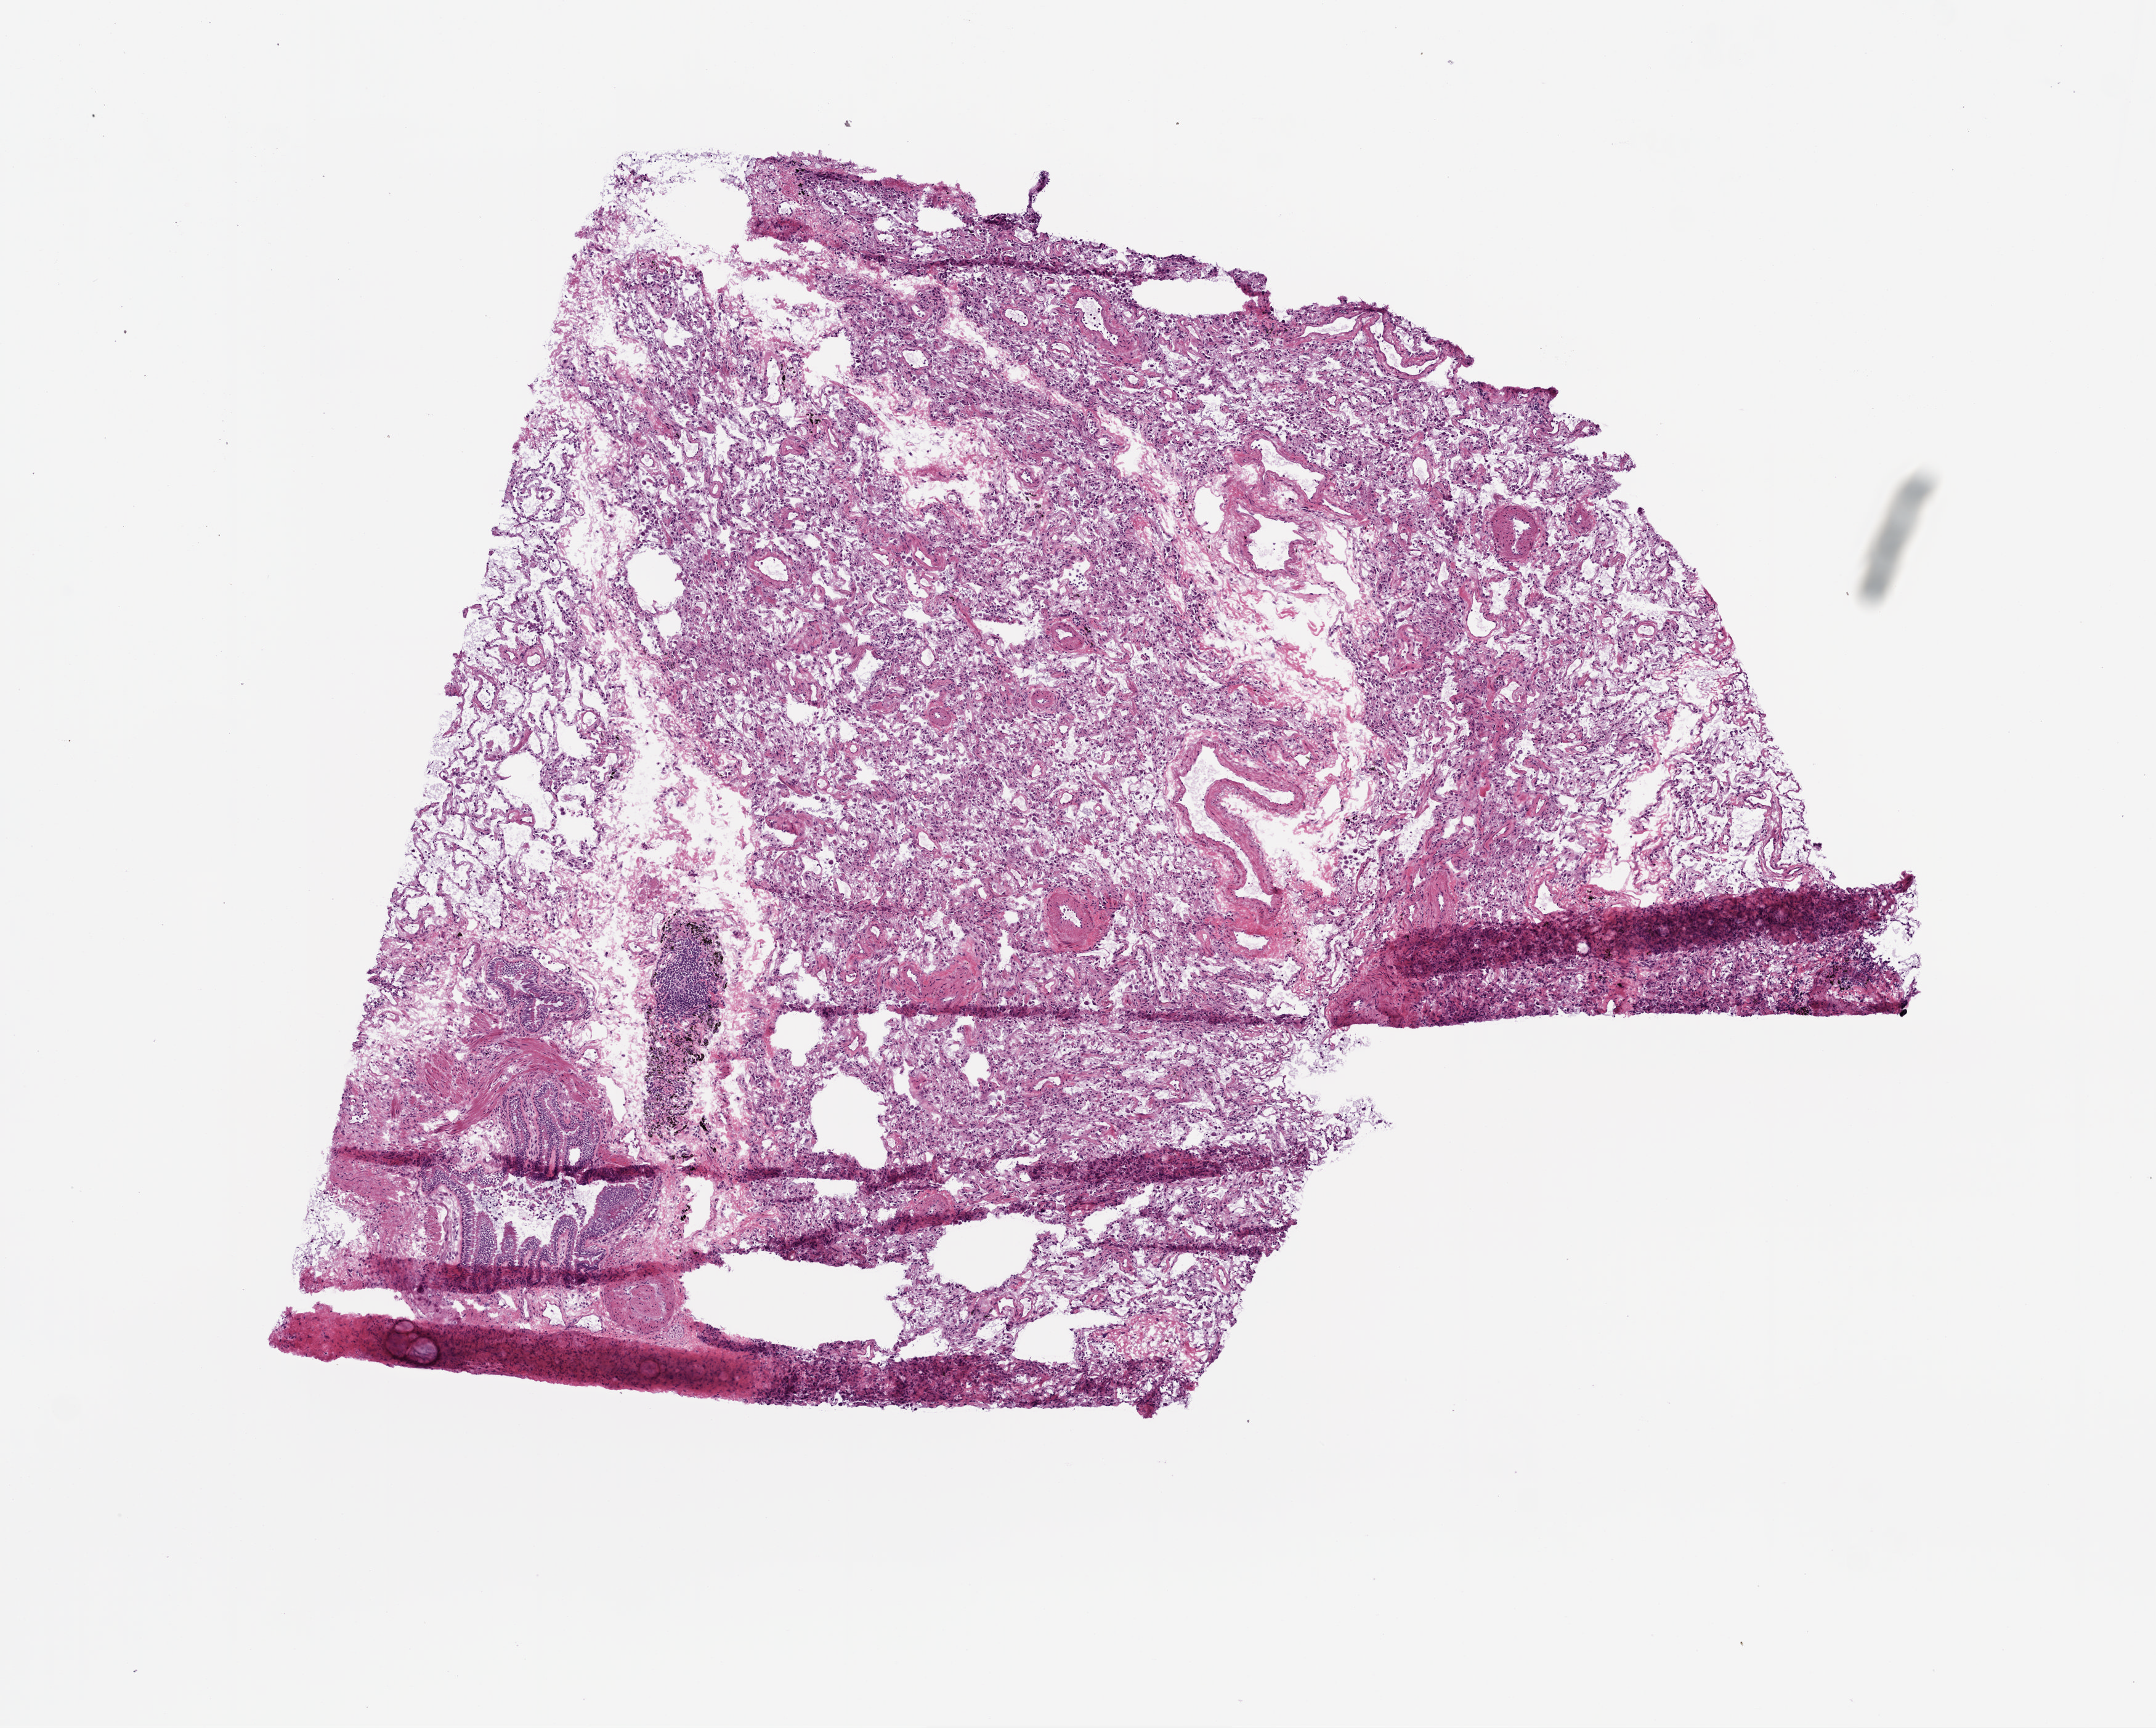
Digitized Hematoxylin and eosin (H&E) stained tissue section (whole slide) — low-resolution overview of the scanned area, about 7.0 x 5.6 mm; frozen section from the top of the tissue portion; solid tissue normal (non-tumour tissue) sample from the lung. Male patient; age at initial diagnosis 78 years.
This section: solid tissue normal sample (biorepository sample class). Patient diagnosis: Squamous cell carcinoma, NOS.